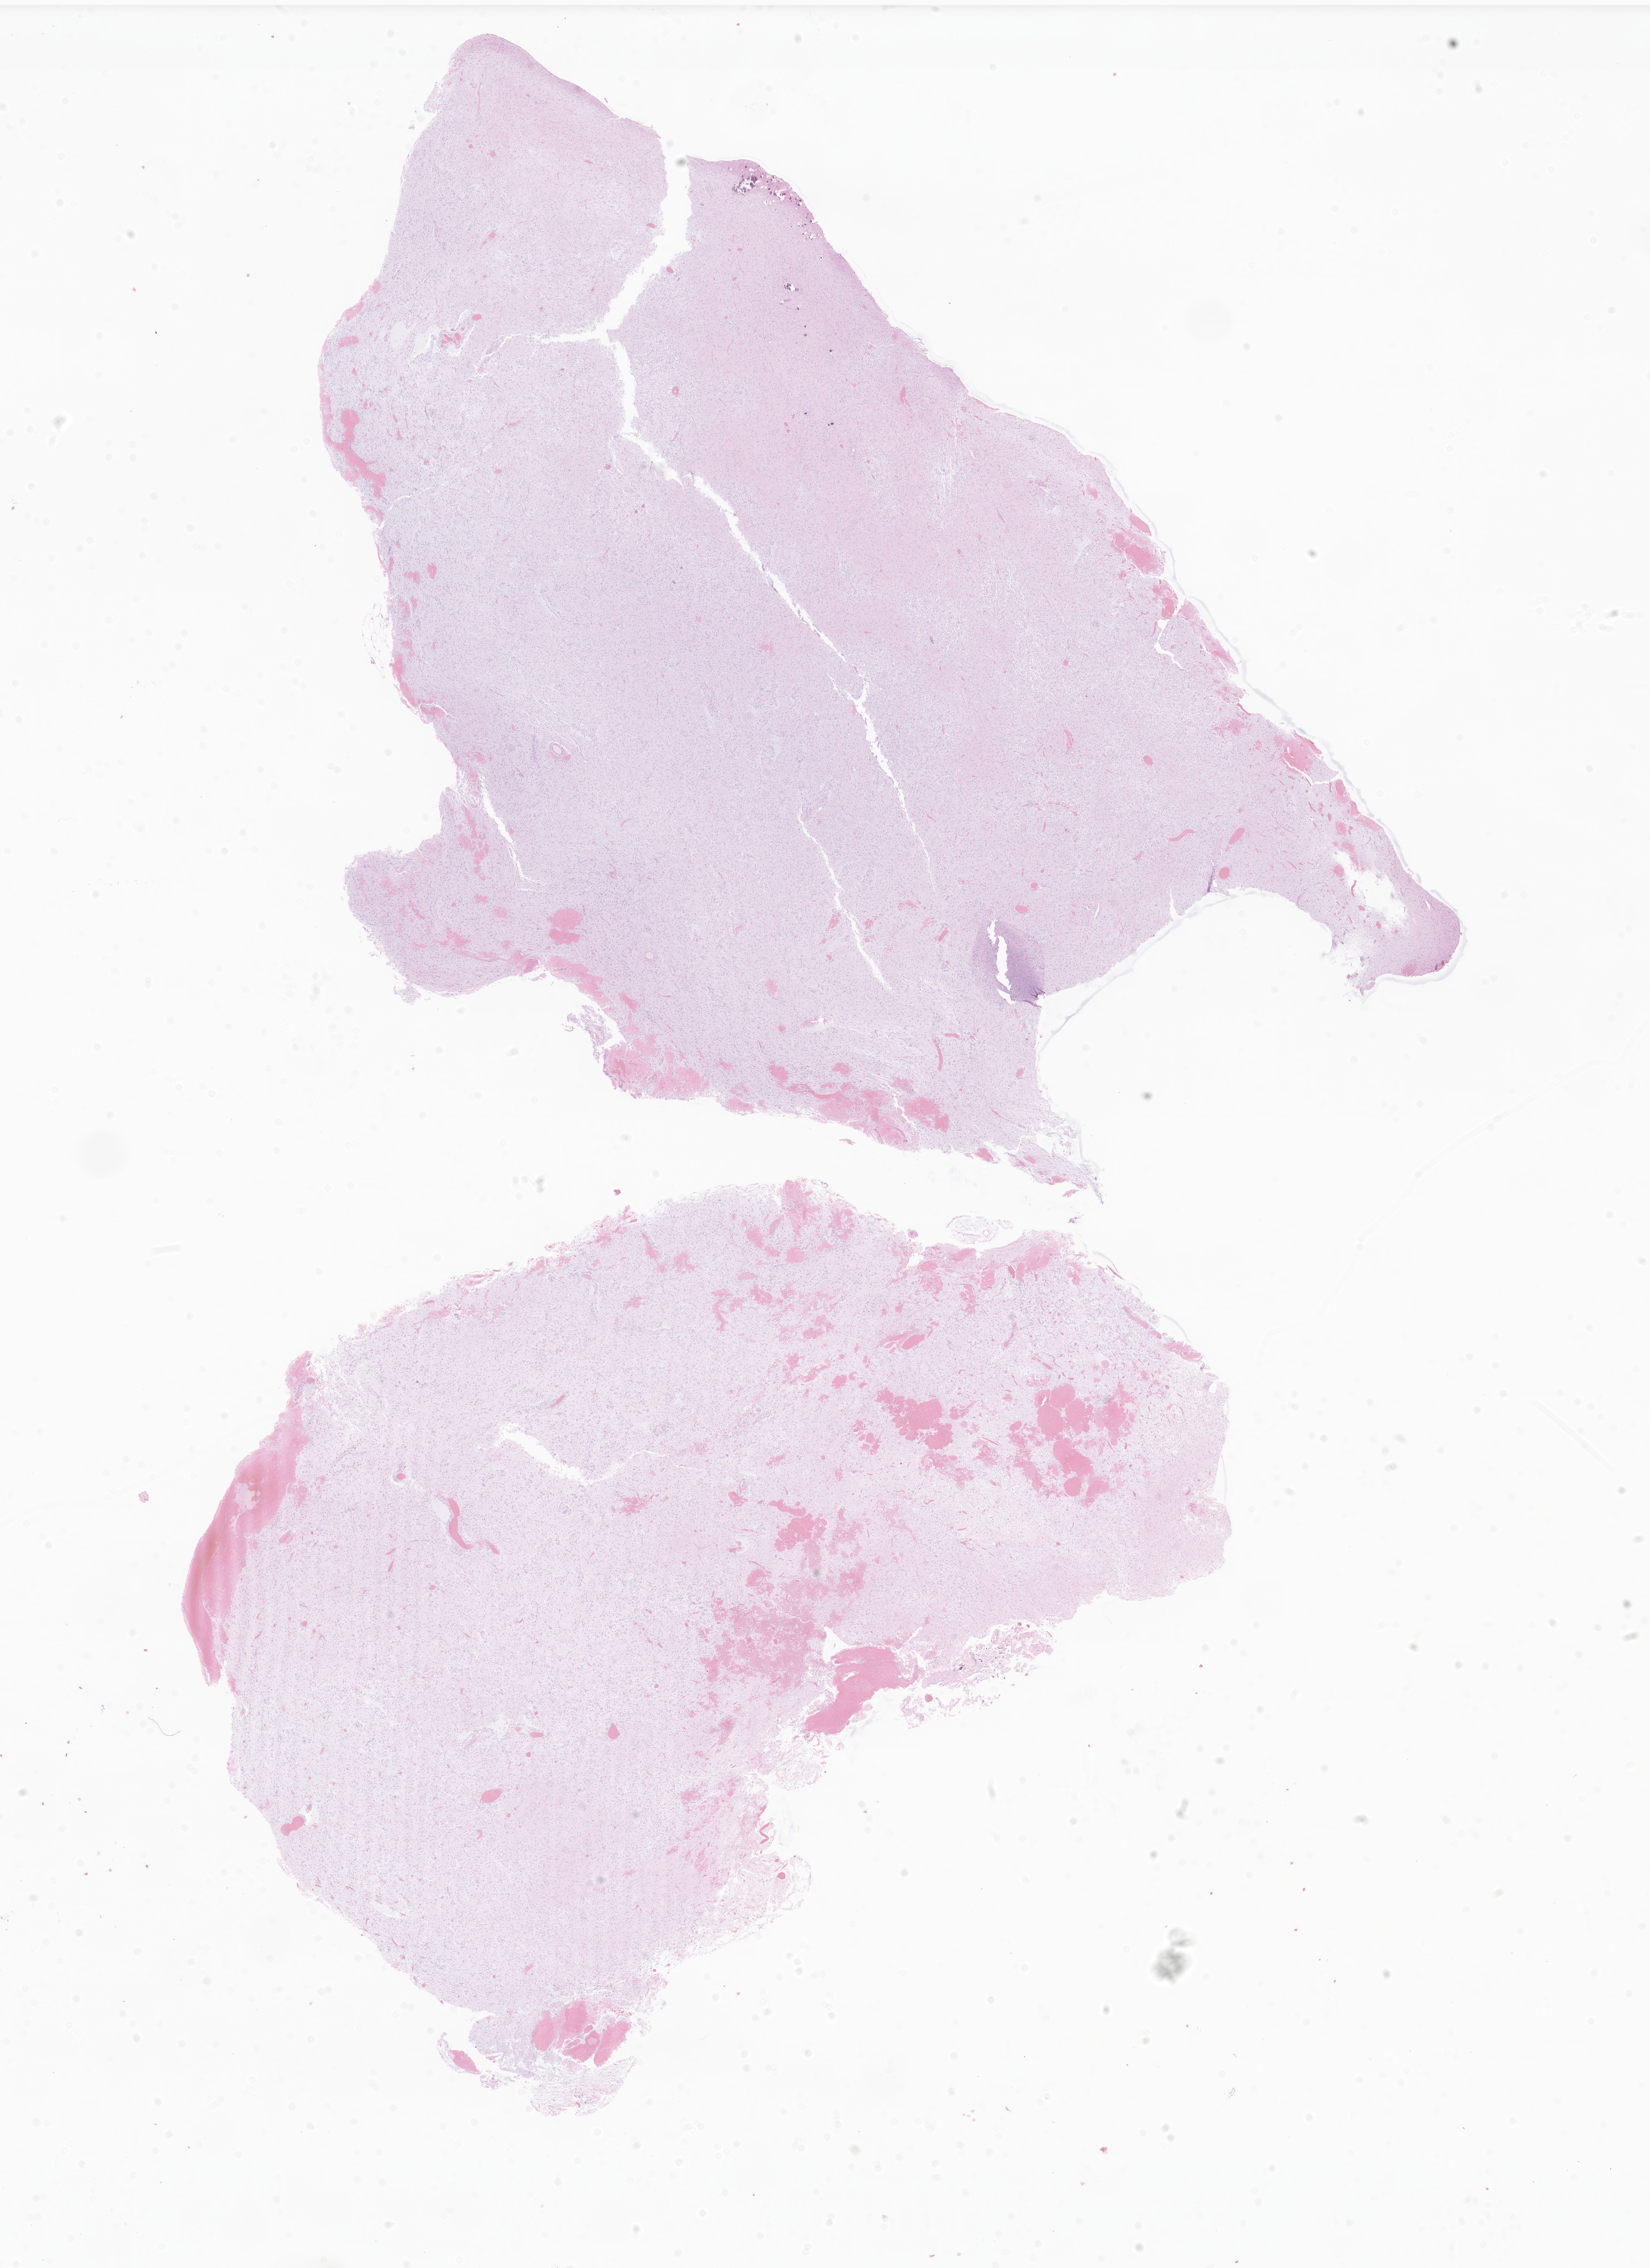
Whole-slide image, hematoxylin and eosin (H&E) stain of tumor tissue from the cerebellum, low-resolution overview of the scanned area, about 16.8 x 23.1 mm. FFPE section. Male patient, age 71 months.
Diagnosis (ICD-O-3 morphology term): Pilocytic astrocytoma.